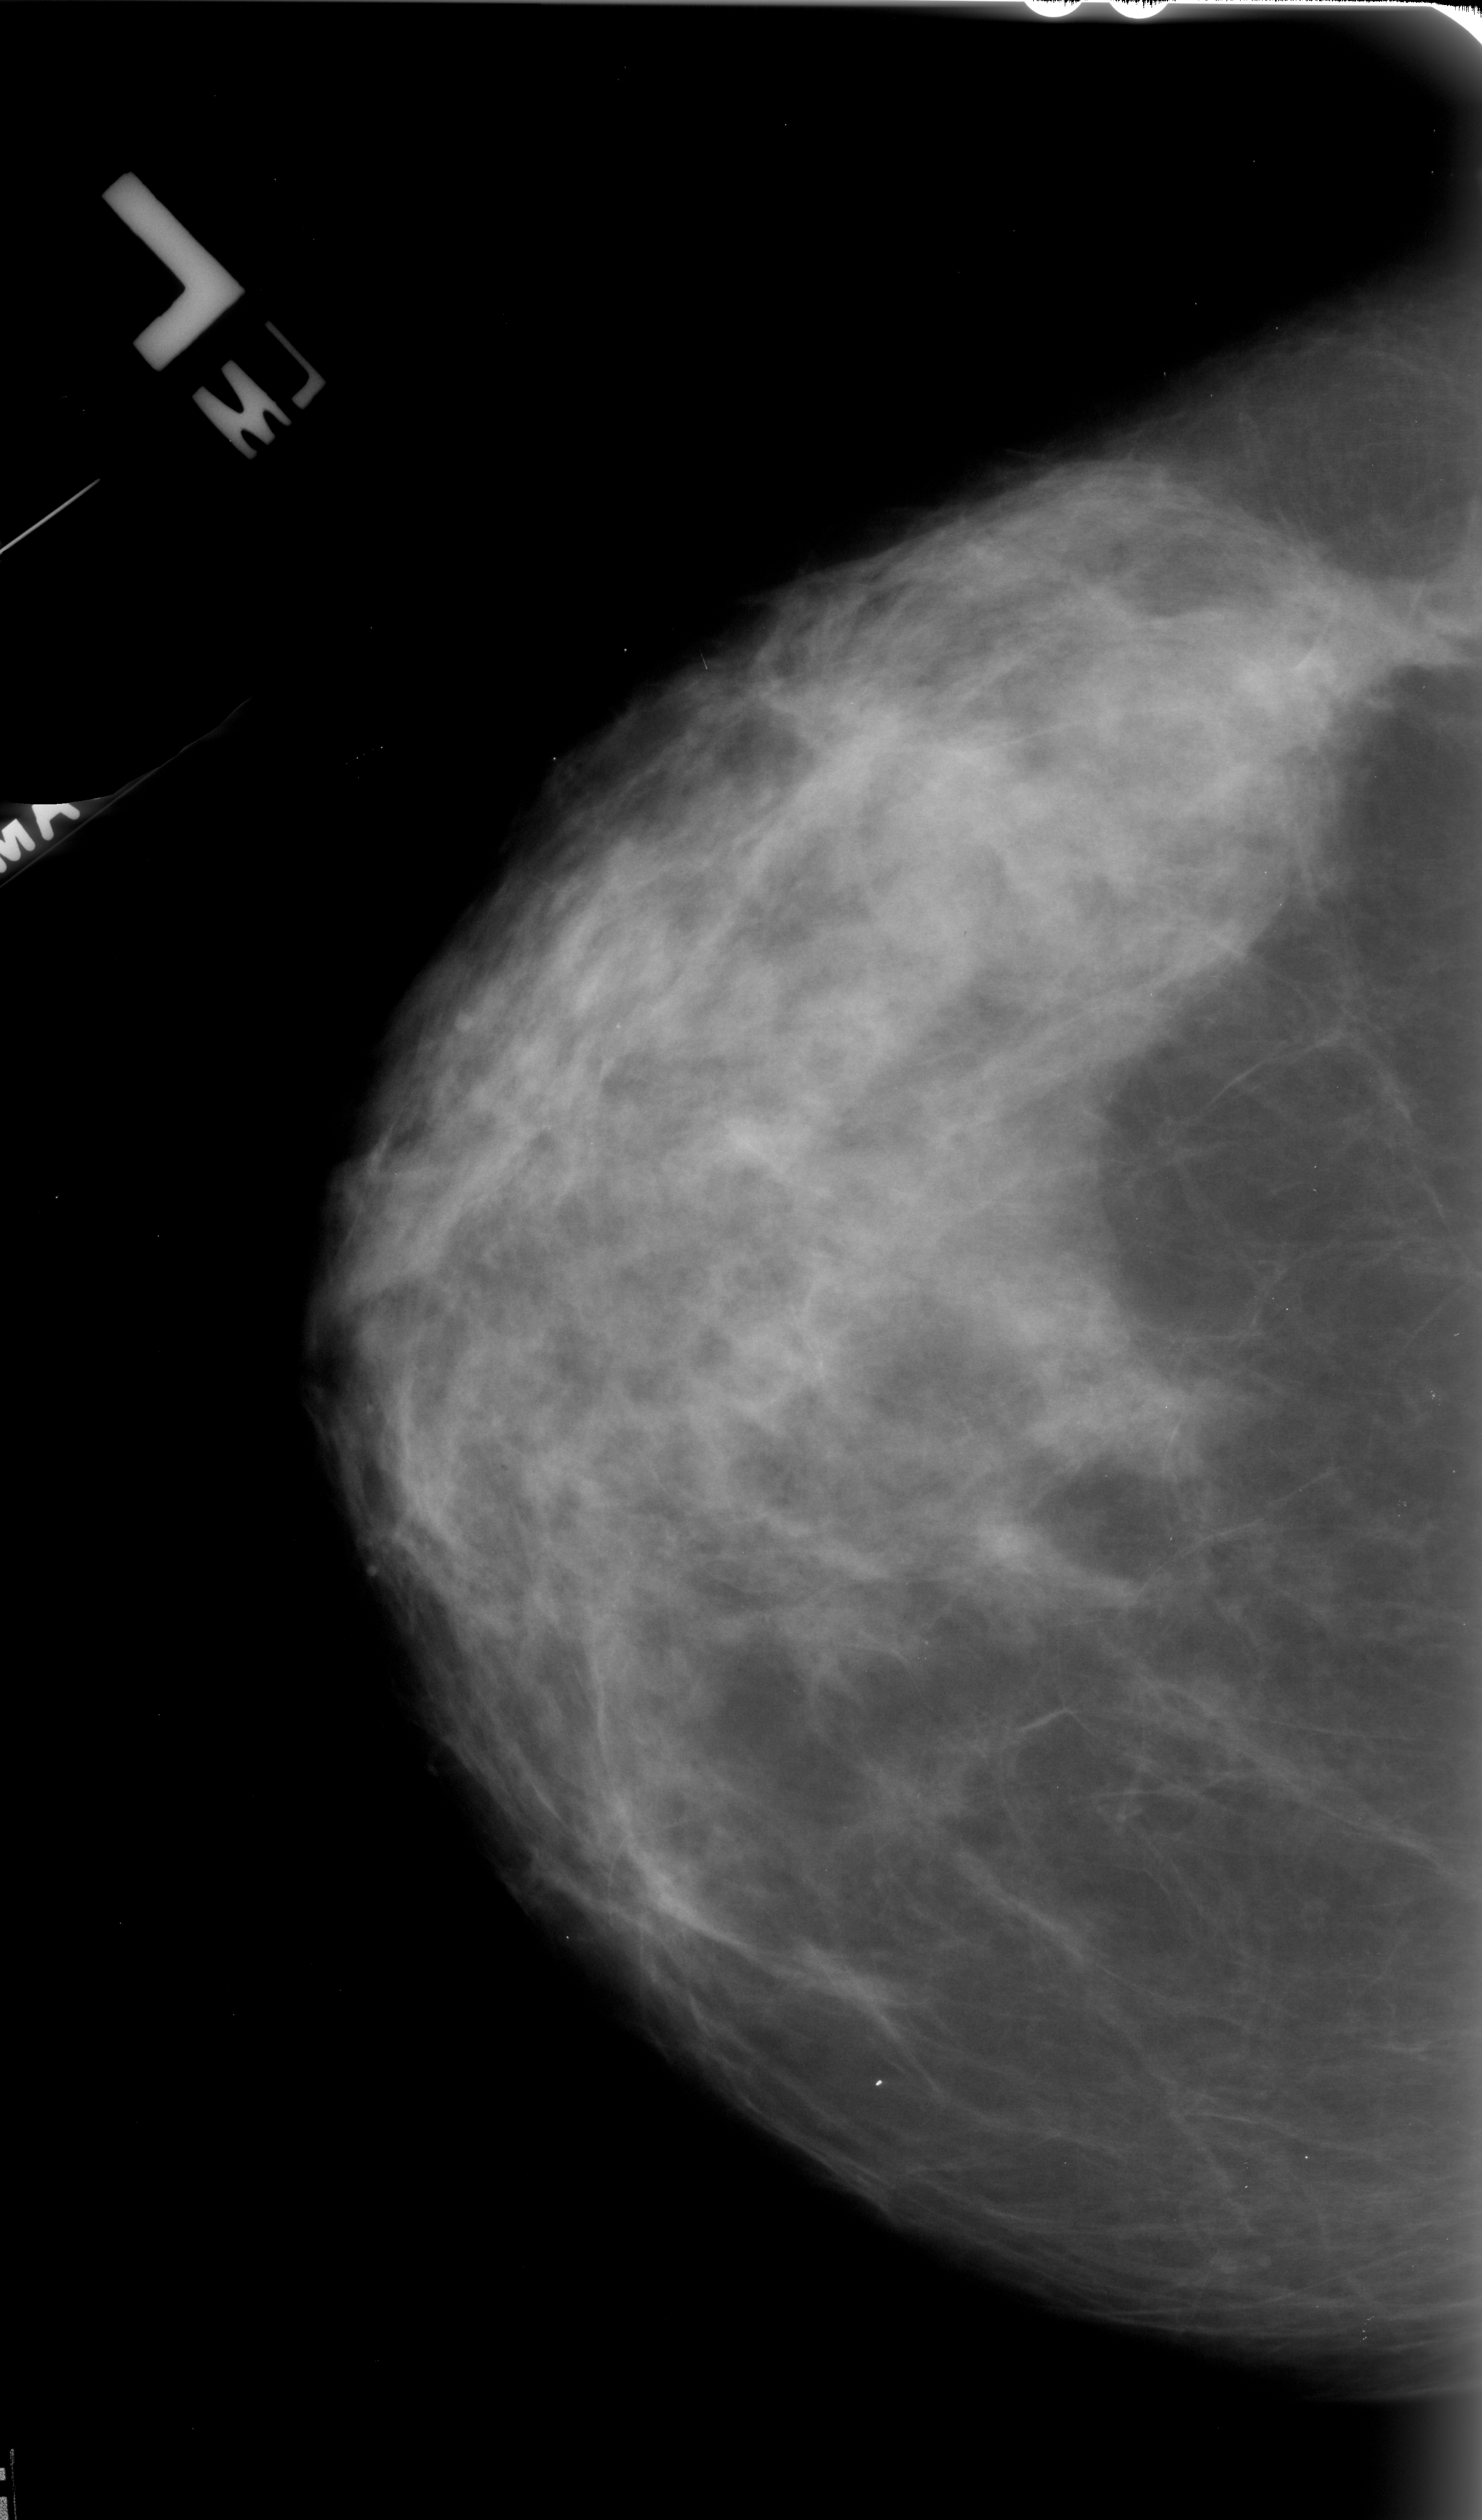
Mammogram (digitized film). Left breast. CC view. Breast composition: heterogeneously dense (BI-RADS density category 3 of 4). 1482 × 2520 image matrix.
Expert-marked regions of interest on this film, with their recorded descriptors:
- mass, shape architectural distortion, margins spiculated; BI-RADS assessment category 5; subtlety rating 2 on a 1 (subtle) to 5 (obvious) scale; pathology result (as recorded, not read from the image): malignant: bounding box (x1, y1, x2, y2) in pixels: (760, 668, 947, 850)